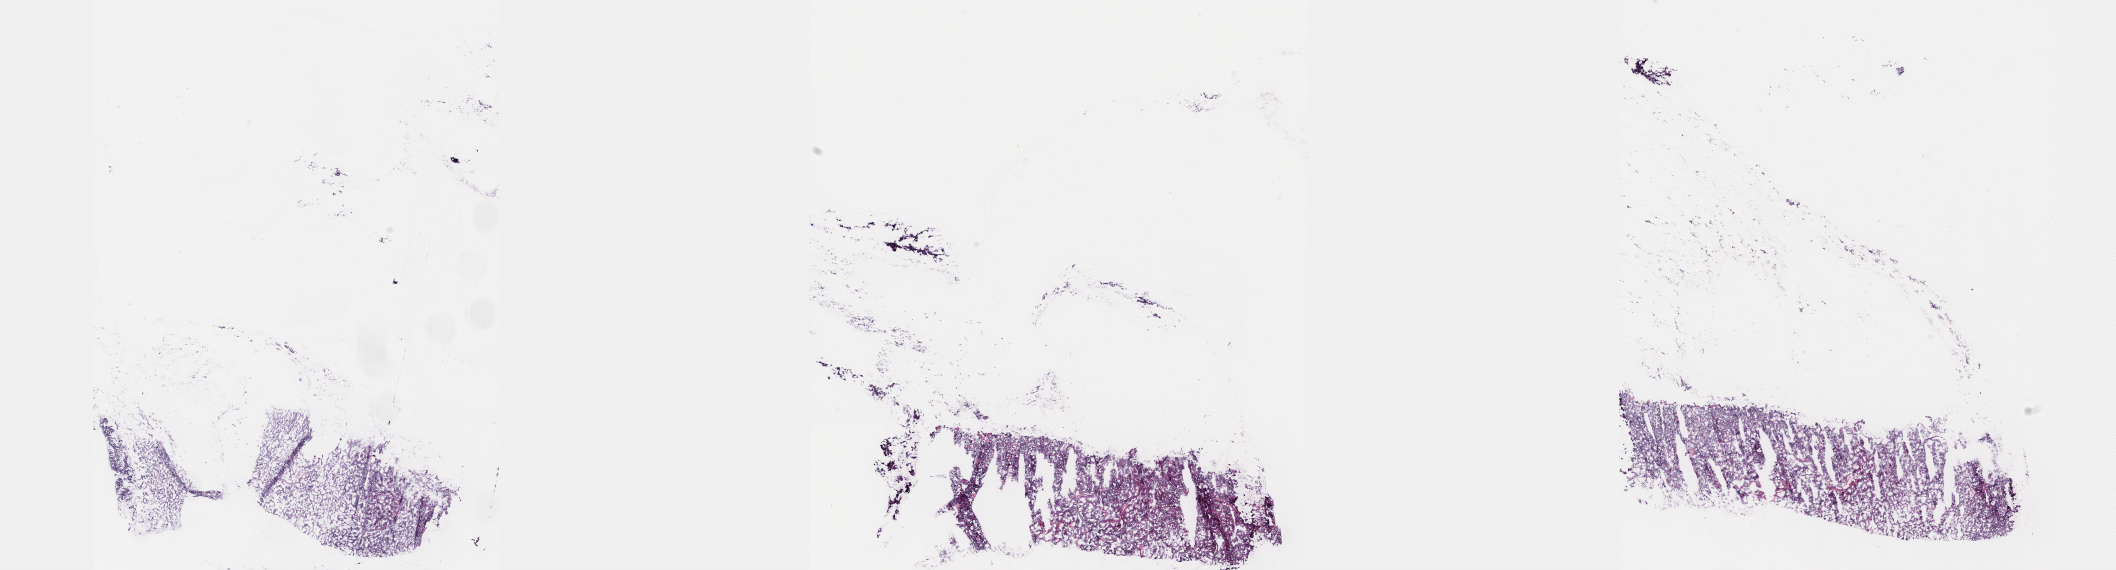
H&E whole-slide image, whole scanned area (about 34.2 x 9.2 mm, from a 40x scan) shown as a low-resolution overview; frozen section; adrenal gland, primary tumour sample. Female, age 64 years at initial diagnosis. Composition of this section per pathologist review: tumour cells 95%, tumour nuclei 95%, normal cells 0%, stromal cells 5%, necrosis 0%. Inflammatory infiltration, as recorded: lymphocyte infiltration 0%, monocyte infiltration 0%, neutrophil infiltration 0%.
- lymph nodes positive (case pathology): 1 of 1 examined
- diagnosis: Pheochromocytoma, malignant